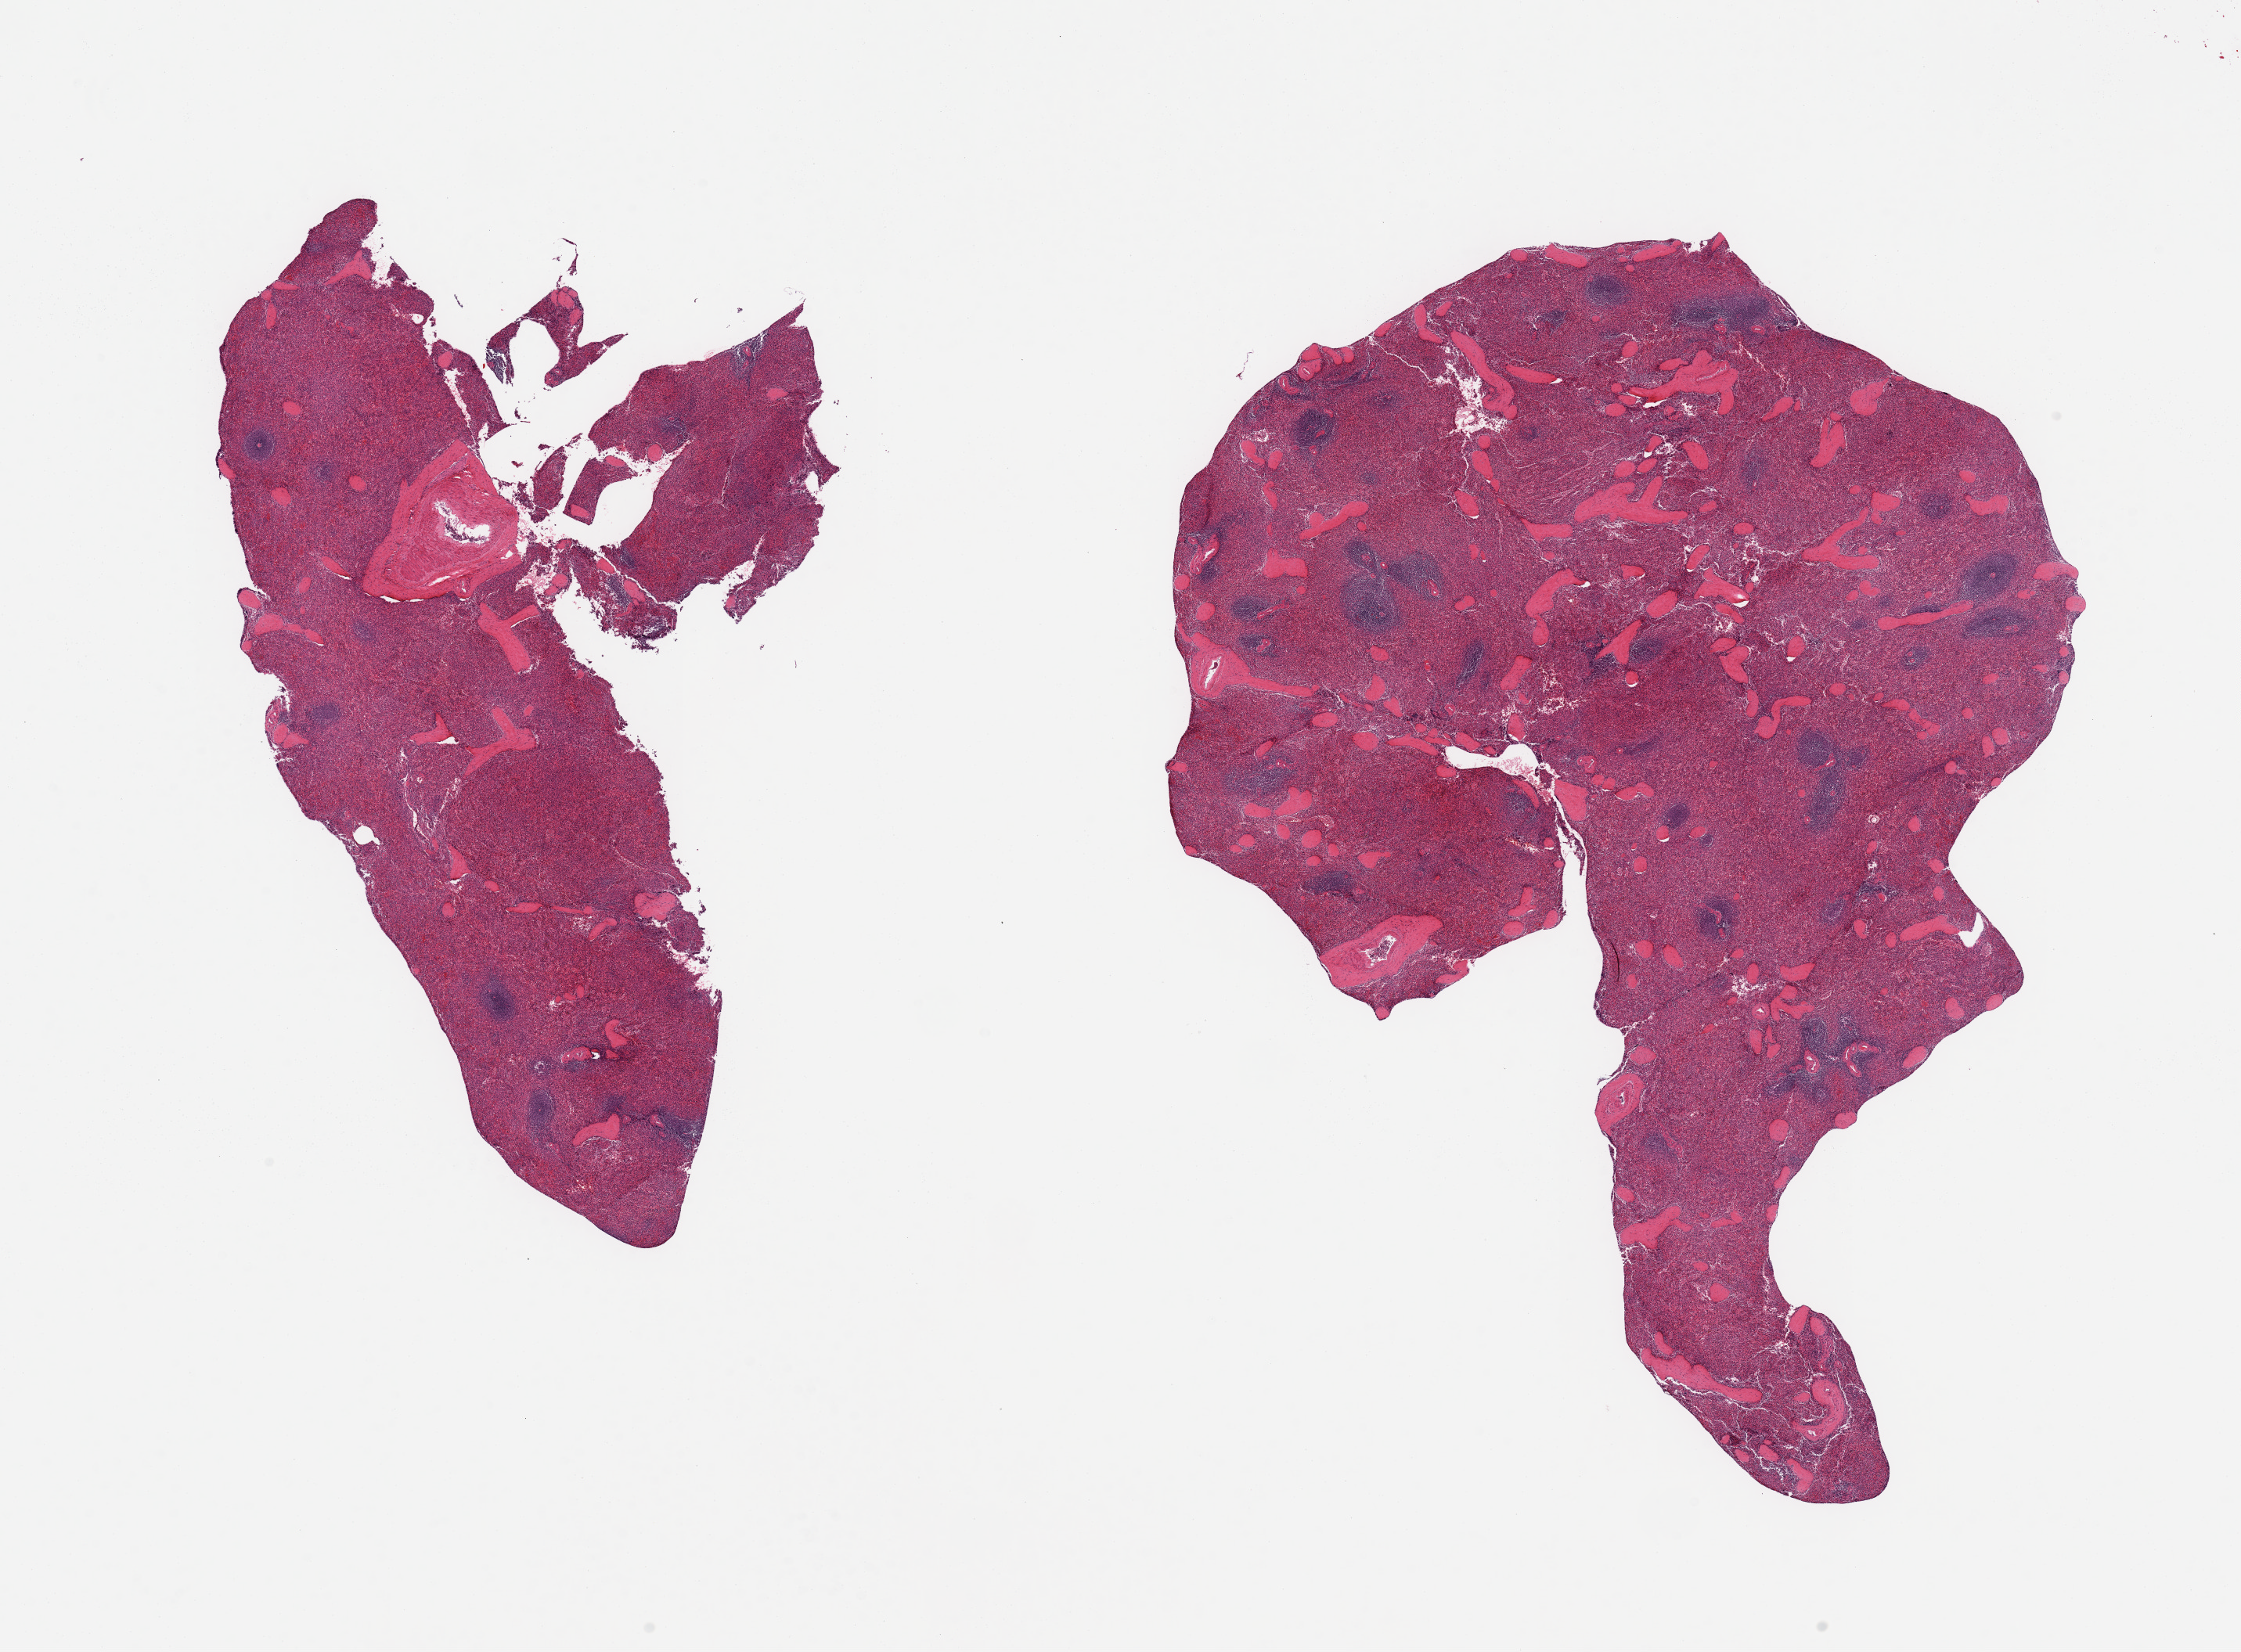
Whole-slide image, hematoxylin and eosin (H&E) stain, brightfield — low-resolution overview of the scanned area, about 22.6 x 16.7 mm, PAXgene-fixed paraffin-embedded (PFPE) section, section of spleen (target tissue), tissue donor sample. Donor sex: male.
Pathologist's review note for this sample: 2 pieces.